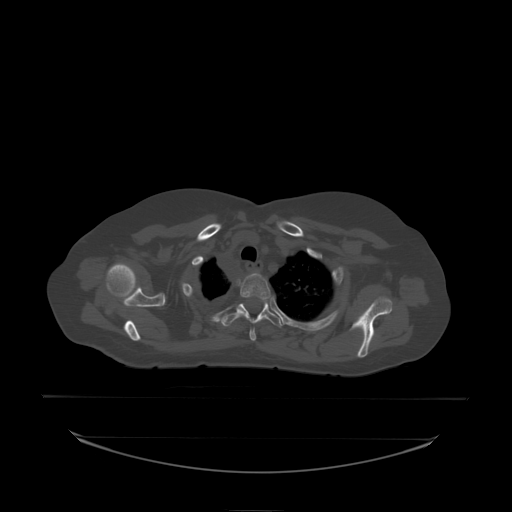
CT including the spine, one axial slice; position 177 of 242 along the scan axis; bone window (W 1800 / L 400 HU); 2.5 mm slice thickness; 512 × 512 image matrix. Female patient, age 53 years. Case-level facts recorded for this patient, not image findings: primary cancer: lung.
Structures marked on this image (semi-automatically segmented with operator editing):
- T2 vertebra: bounding box <238,273,272,338> (left, top, right, bottom; pixels)
- T3 vertebra: <222,303,284,328>